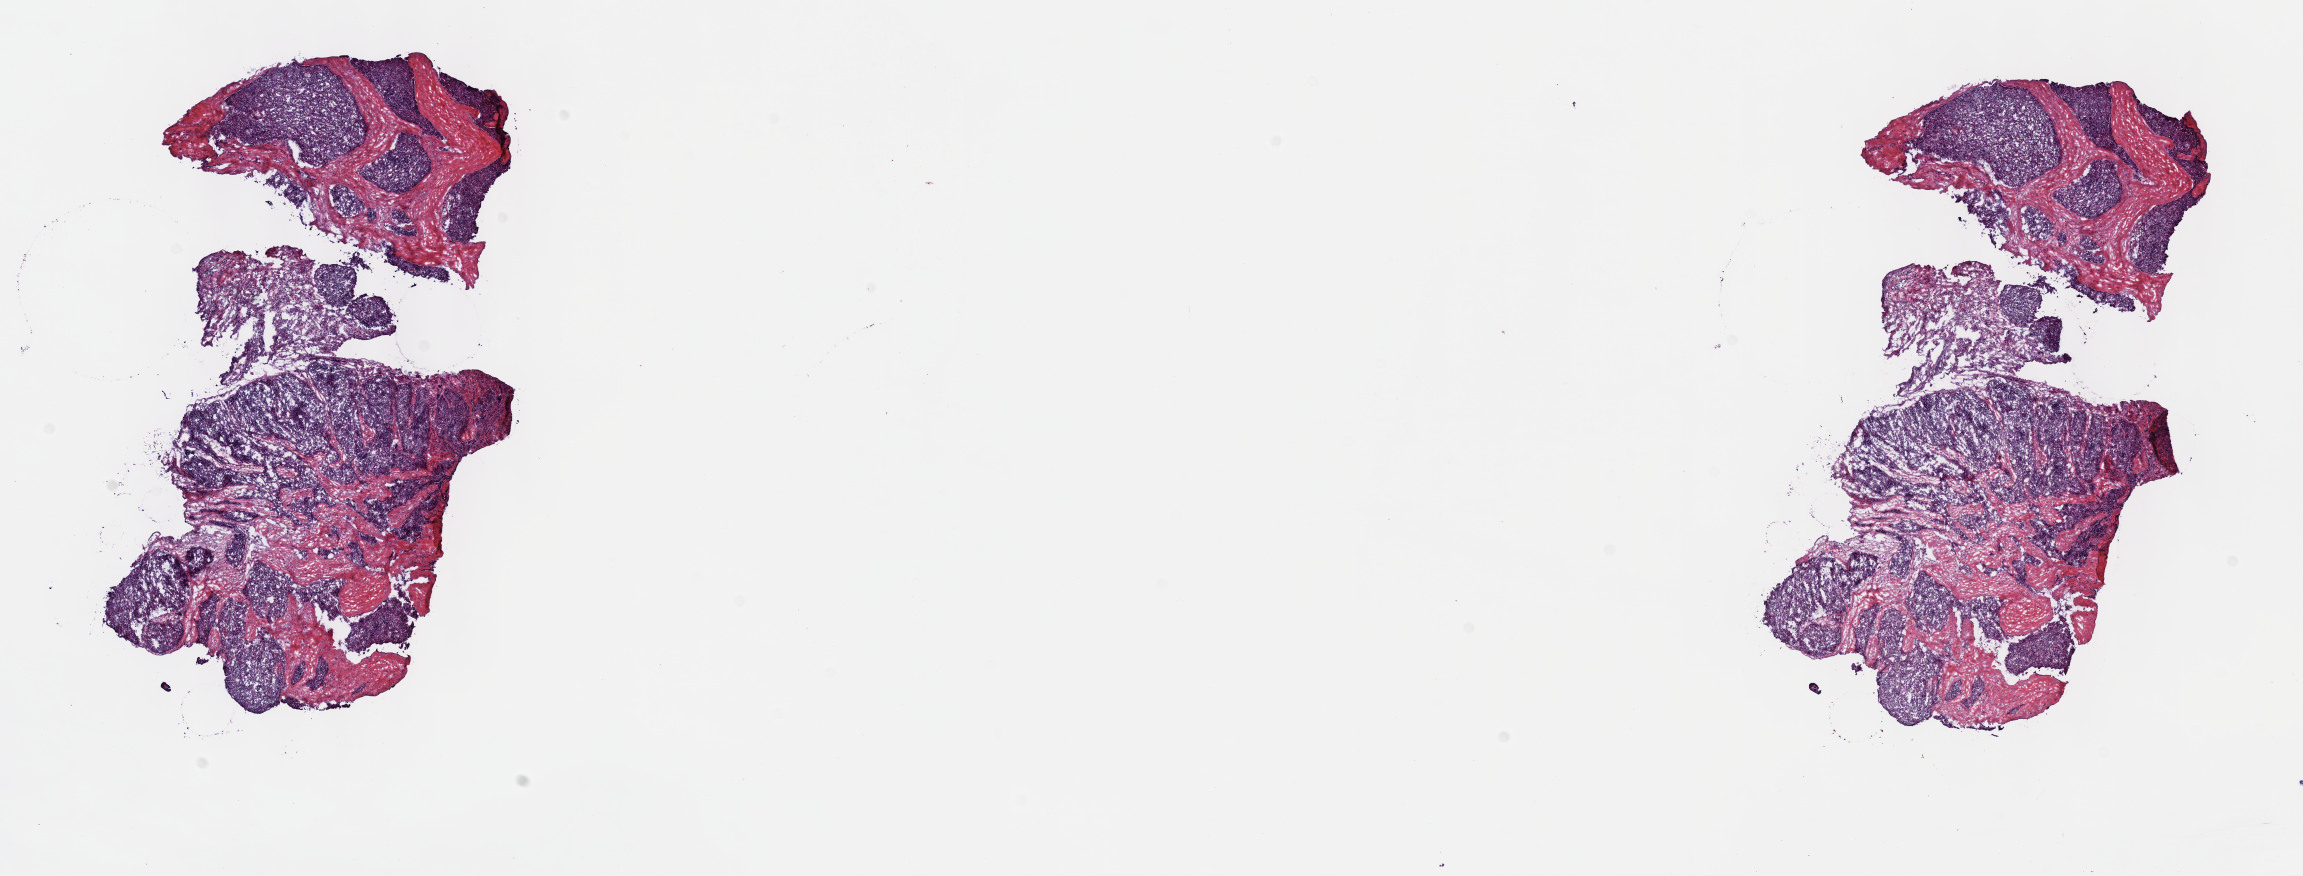
H&E whole-slide image, shown as a low-resolution overview of the whole scanned area (about 18.6 x 7.1 mm, from a 40x scan); frozen section; primary tumour sample from the thymus. Female, age 51 years at initial diagnosis. Pathologist review of this section (percent, as recorded): tumour cells 50%, tumour nuclei 60%, normal cells 0%, stromal cells 50%, necrosis 0%. Infiltration values recorded for this section: lymphocyte infiltration 0%, monocyte infiltration 0%, neutrophil infiltration 0%.
Diagnosis: Thymoma, type B3, malignant.